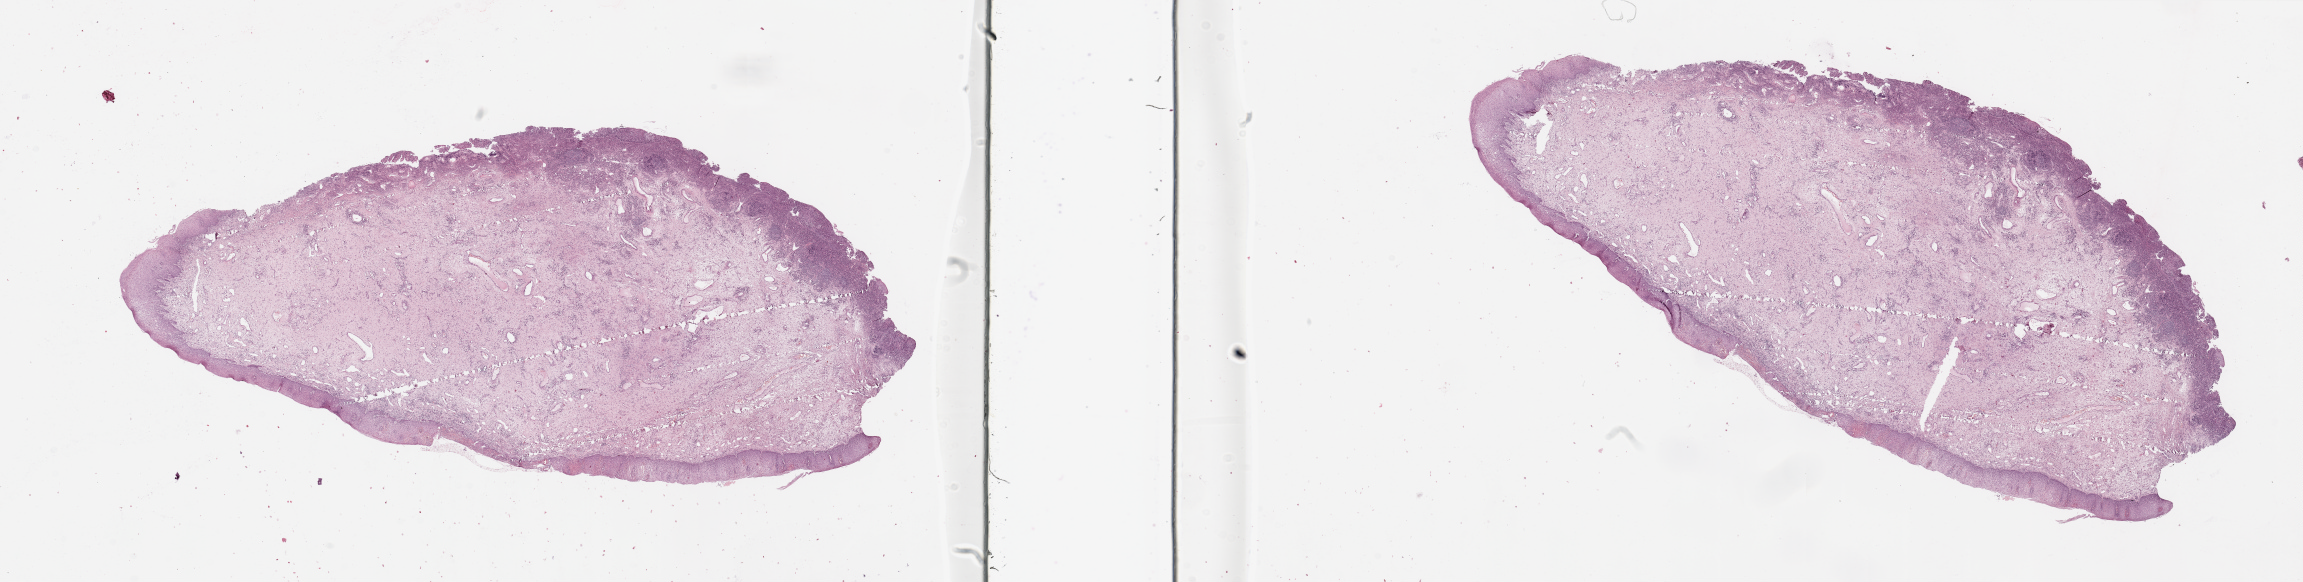
Whole-slide histology image, H&E-stained, low-resolution overview of the scanned area, about 36.4 x 9.2 mm (from a 20x scan); normal (non-tumour) tissue sample, sampled site: sinus. Patient: male, age 64 years.
This section: normal (non-tumour) tissue from the same patient. Patient diagnosis: Squamous cell carcinoma, NOS (head, face or neck, NOS).